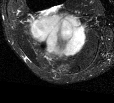
MRI of an extremity soft-tissue mass, one axial slice. Position 32 of 44 along the scan axis. T2-weighted fat-saturated. MR volume resampled by the dataset authors to the PET/CT grid (not the native acquisition matrix). 3.27 mm slice thickness. 114 × 103 image matrix, field of view 111 × 101 mm. Female patient. Case-level facts recorded for this patient, not image findings: histological type: liposarcoma; site of the primary tumour: right thigh.
Annotated regions visible in this slice (expert contour drawn on MRI and transferred to this co-registered scan by the dataset authors):
- gross tumour volume (mass): bounding box <27,11,87,60> (left, top, right, bottom; pixels)